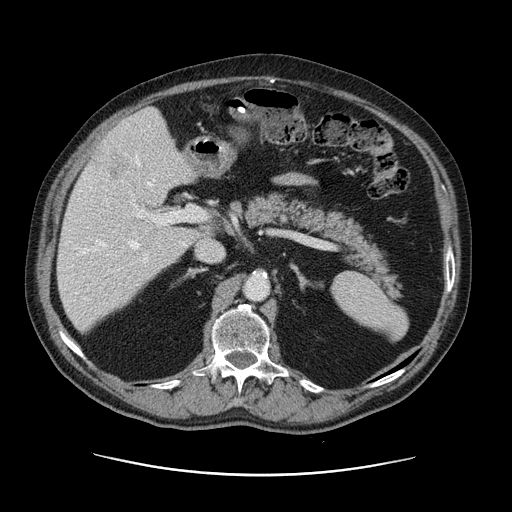
Contrast-enhanced abdominal CT, one axial slice. Slice 73 of 141 in the series (ordered by position). 120 kVp. Intravenous contrast given. Soft-tissue window (W 400 / L 40 HU). 512 × 512 image matrix. Male patient, age 72 years. From the clinical record (not read from this slice): diagnosis: colorectal cancer liver metastases, imaged before liver resection.
Structures marked on this image (outlined manually by an expert reader):
- hepatic veins: box from (x=95, y=156) to (x=153, y=249) px
- liver: (x=58, y=109)–(x=202, y=331)
- planned liver remnant (the part of the liver to remain after resection): (x=58, y=175)–(x=204, y=331)
- portal vein (with intrahepatic branches): (x=83, y=199)–(x=203, y=300)
- liver metastasis: (x=109, y=170)–(x=118, y=178)